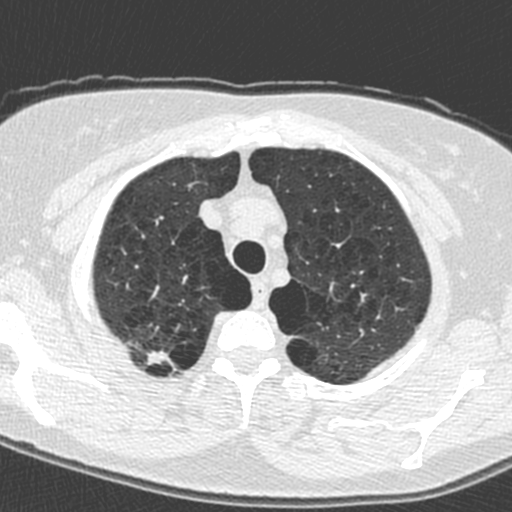
Low-dose screening chest CT, axial slice, first (baseline) screen, lung window (W 1500 / L -600 HU), standard (soft-tissue) reconstruction kernel (C), slice 21 of 224 in the series, 512 × 512 image matrix, field of view 278 × 278 mm. Female participant, aged 59 years at enrolment. Current smoker at enrolment.
• Expert-annotated lung lesion, box from (x=132, y=334) to (x=177, y=377) px.
• Screening reader's record for this exam: no non-calcified nodule ≥4 mm recorded.
• Official screen result: negative screen, minor abnormalities not suspicious for lung cancer.
• Lung cancer was diagnosed 881 days after this screen: adenocarcinoma, NOS, right upper lobe, poorly differentiated (G3), stage IA (AJCC 6th edition), 20 mm at pathology.